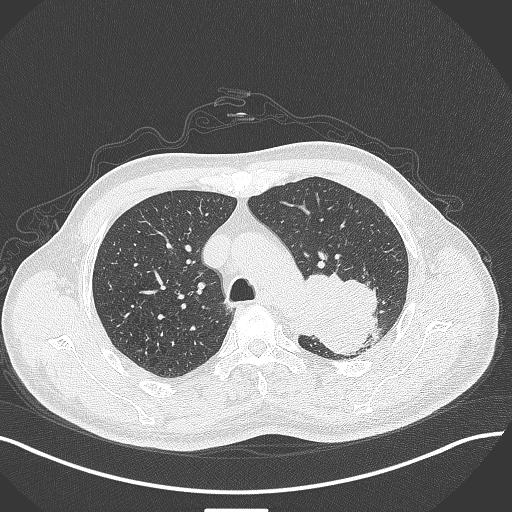
Chest CT, one axial slice. Slice 312 of 429 in the series (ordered by position). Lung window (W 1500 / L -600 HU). 512 × 512 image matrix, field of view 400 × 400 mm. Male patient, age 55 years. From the clinical record (not read from this slice): clinical TNM (as recorded): T3 N0 M1c.
Structures marked on this image (bounding box drawn by a radiologist):
- lung tumour (recorded histology: adenocarcinoma): bounding box (x1, y1, x2, y2) in pixels: (299, 271, 383, 357)